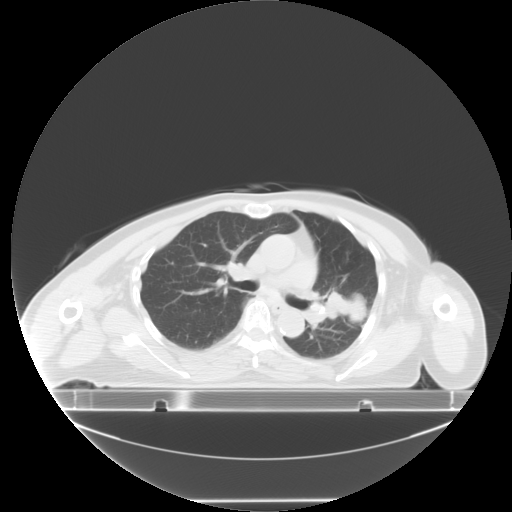
Chest CT, one axial slice; slice 3 of 24 in the series (ordered by position); lung window (W 1500 / L -600 HU); 5 mm slice thickness; 512 × 512 image matrix, field of view 500 × 500 mm. Female patient, age 74 years. Case-level facts recorded for this patient, not image findings: clinical TNM (as recorded): T3 N1 M1c; histopathological grade: G3.
Annotated regions visible in this slice (bounding box drawn by a radiologist):
- lung tumour (recorded histology: small cell carcinoma): bounding box (x1, y1, x2, y2) in pixels: (326, 289, 370, 327)